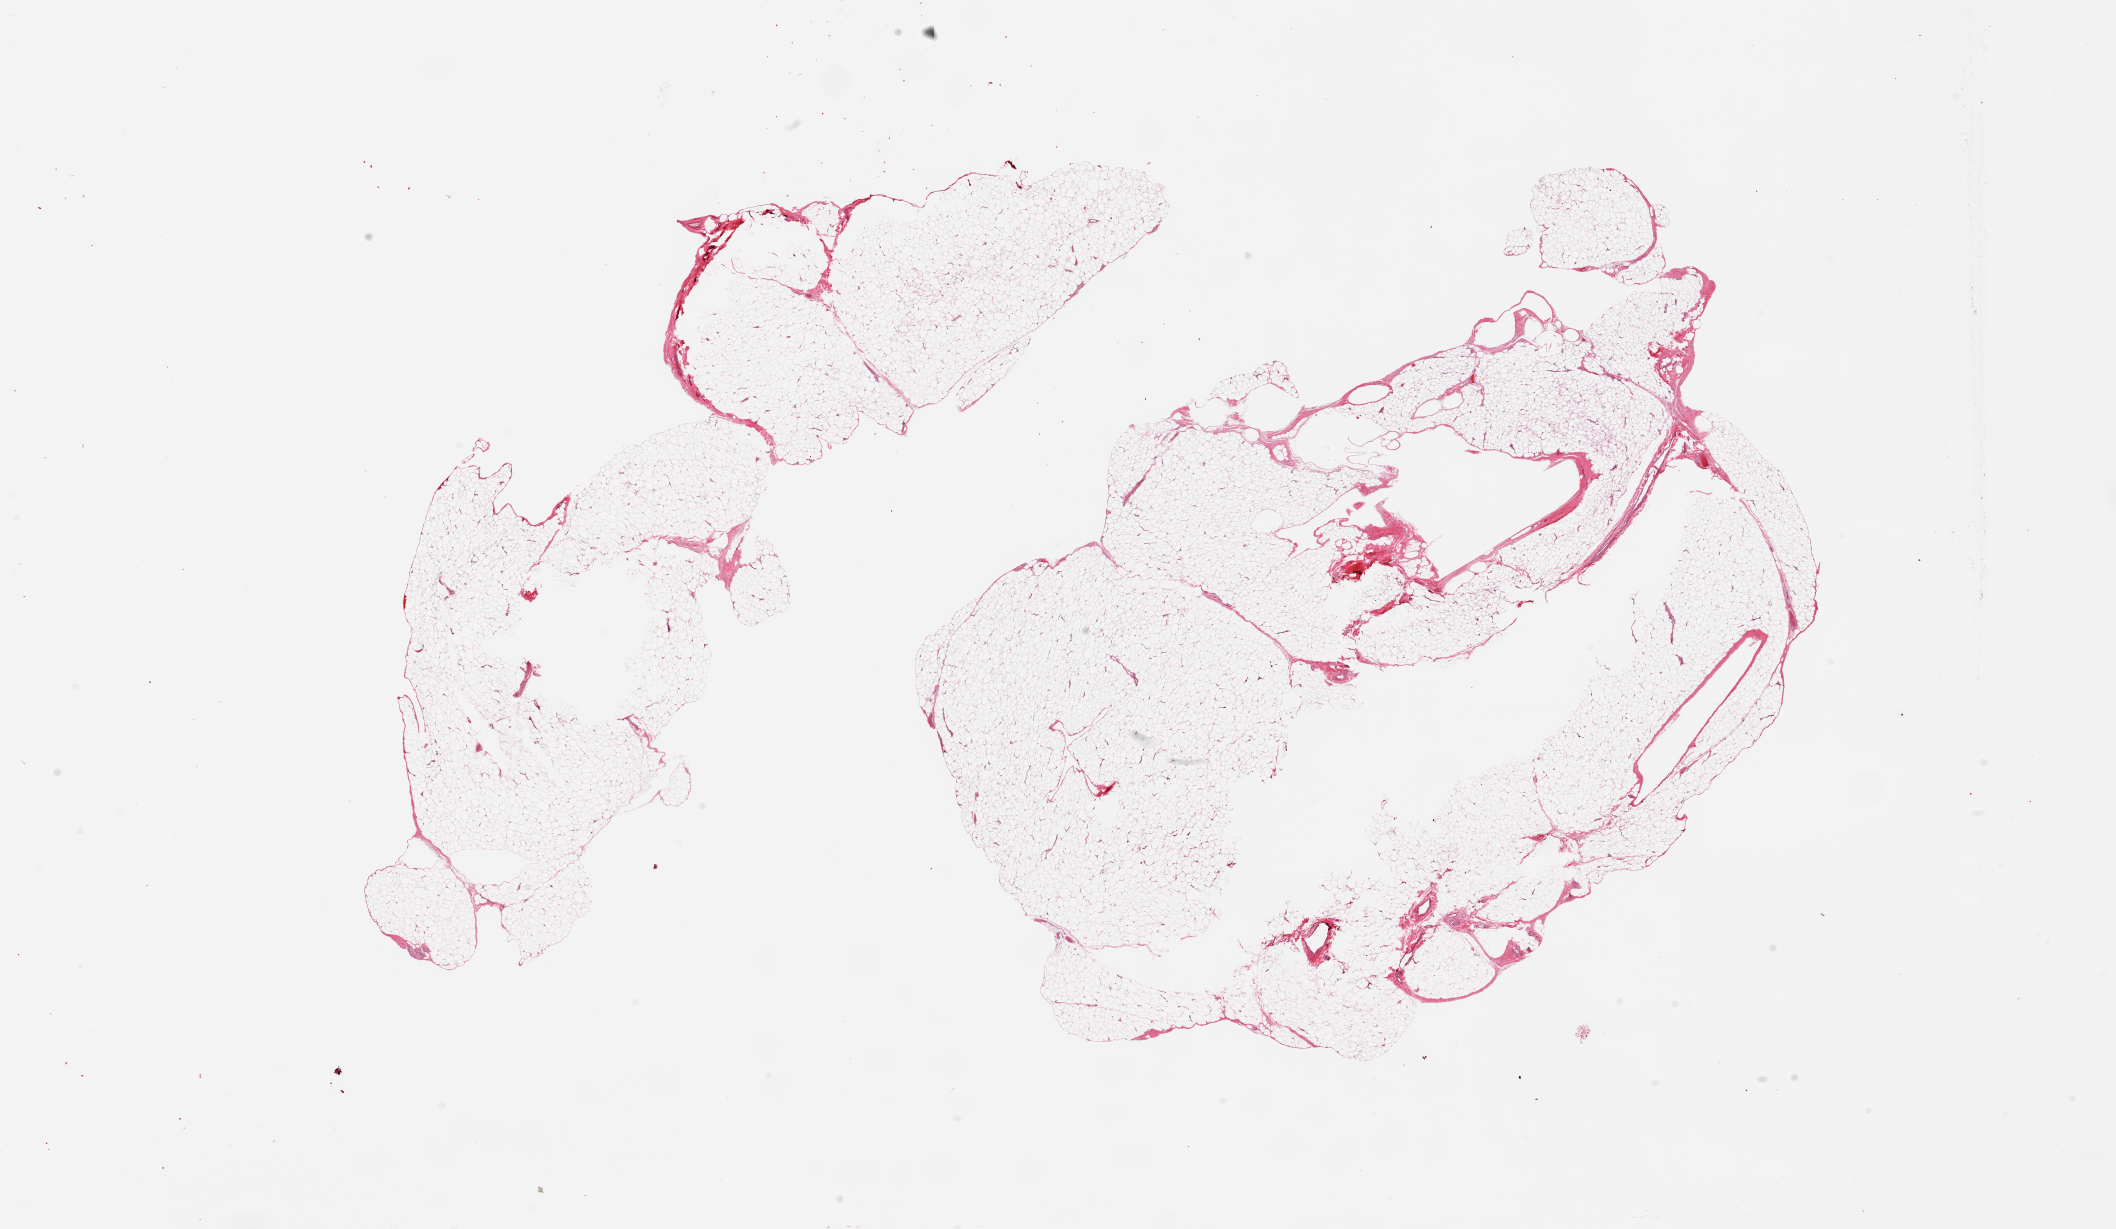
Whole-slide image, hematoxylin and eosin (H&E) stain, shown as a low-resolution overview of the whole scanned area (about 33.5 x 19.4 mm). PAXgene-fixed paraffin-embedded (PFPE) section. Target tissue: adipose tissue. Donor tissue sample. Donor: male.
Pathologist's review note for this sample: 2 pieces.